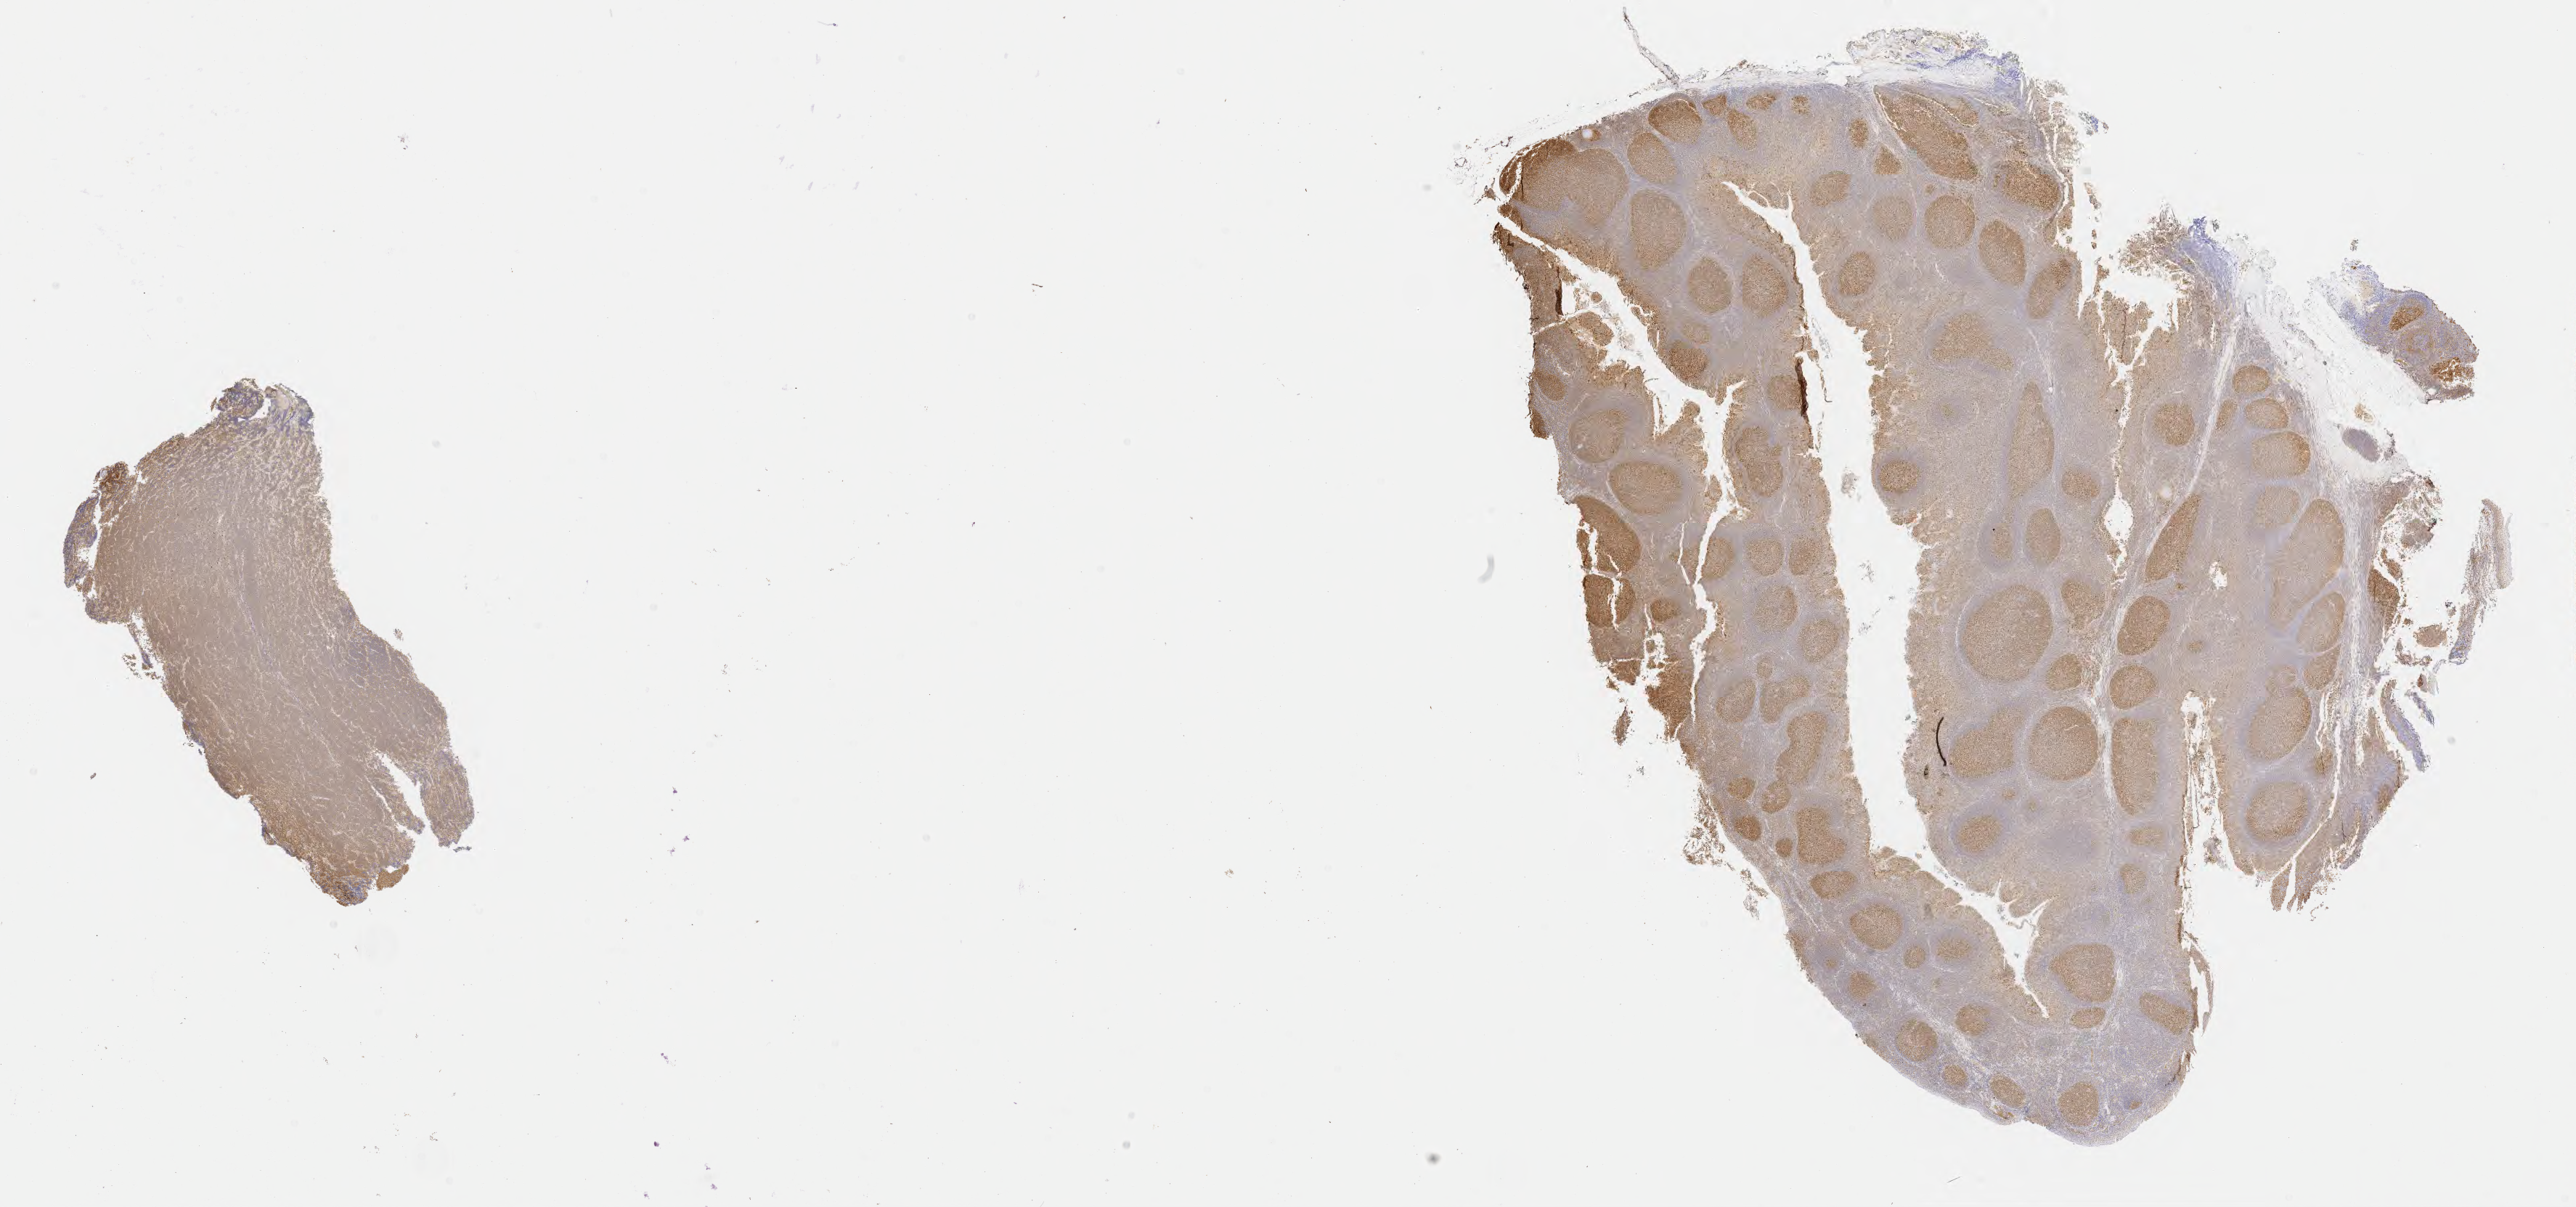
IHC for BCL6, whole-slide image, whole scanned area (about 28.7 x 13.4 mm) shown as a low-resolution overview. Tumor tissue. Site: cranium. Patient: male, aged 11.
Diagnosis: Diffuse large B-cell lymphoma, NOS.